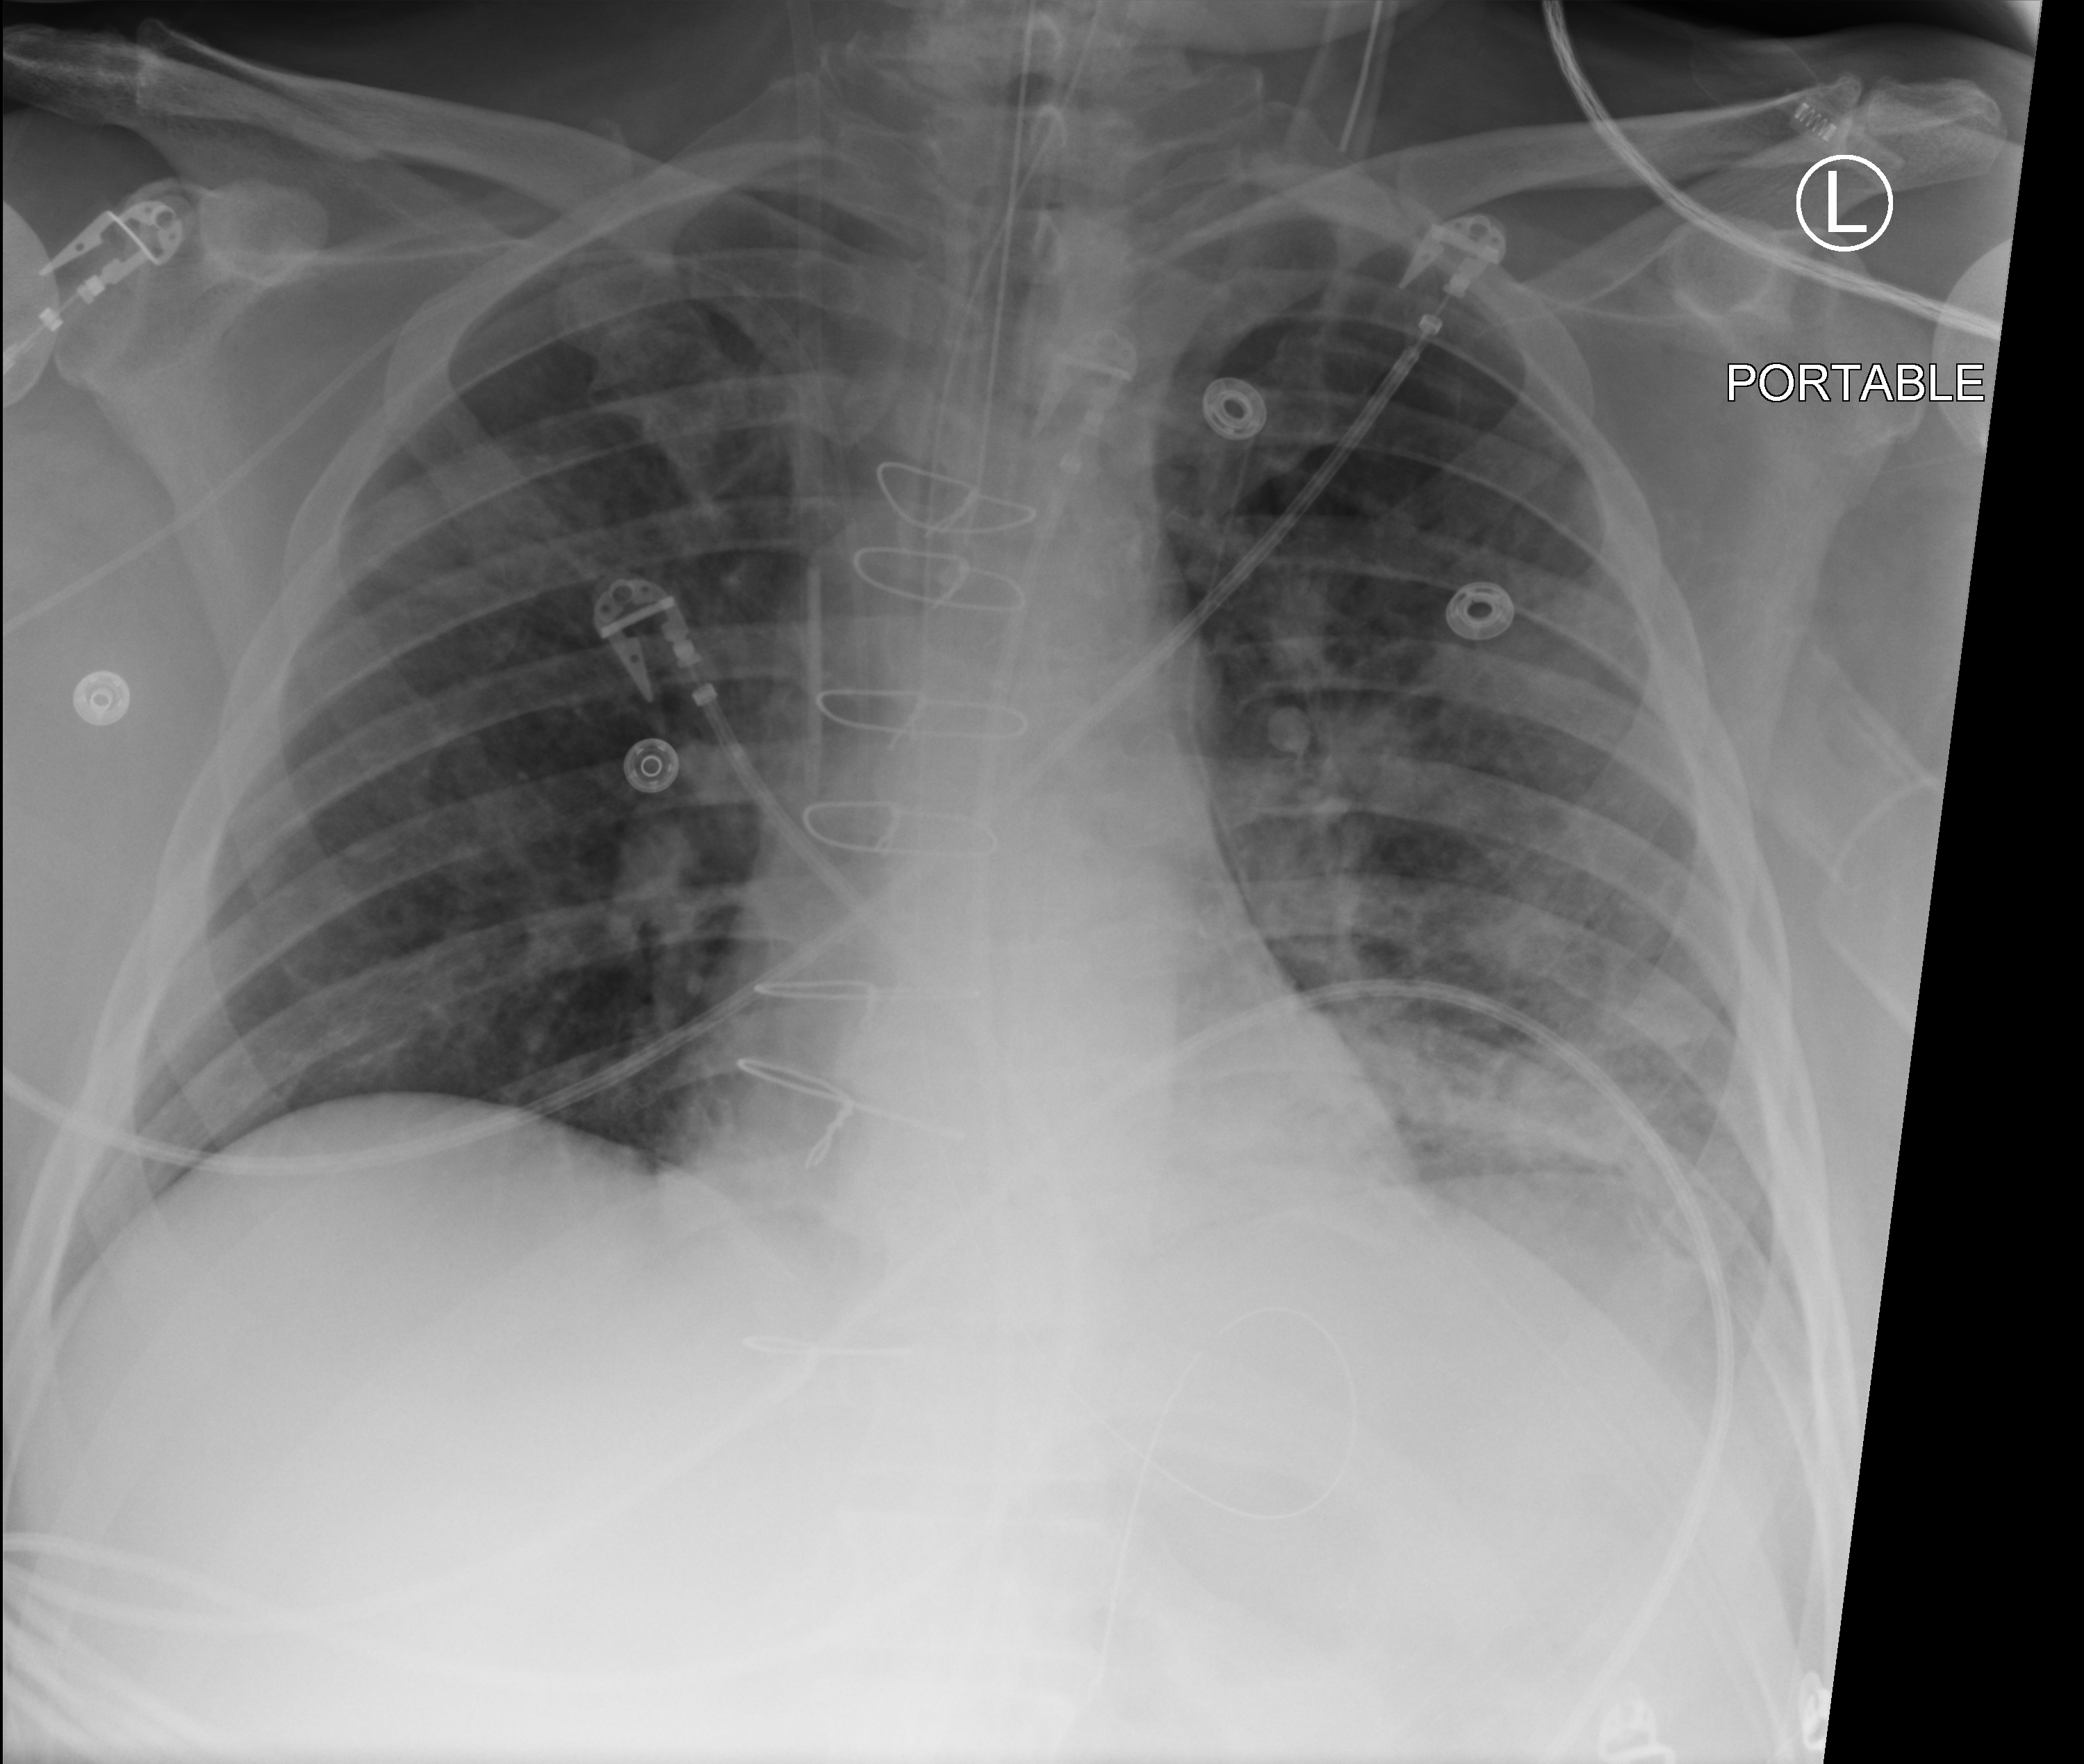
Bedside chest radiograph (computed radiography), anteroposterior (AP) projection. Patient hospitalised with COVID-19; male, aged 60–74 years.
From the hospital-stay record, not from the radiograph (when in the stay this image was taken is not recorded): smoking status (admission record): former.